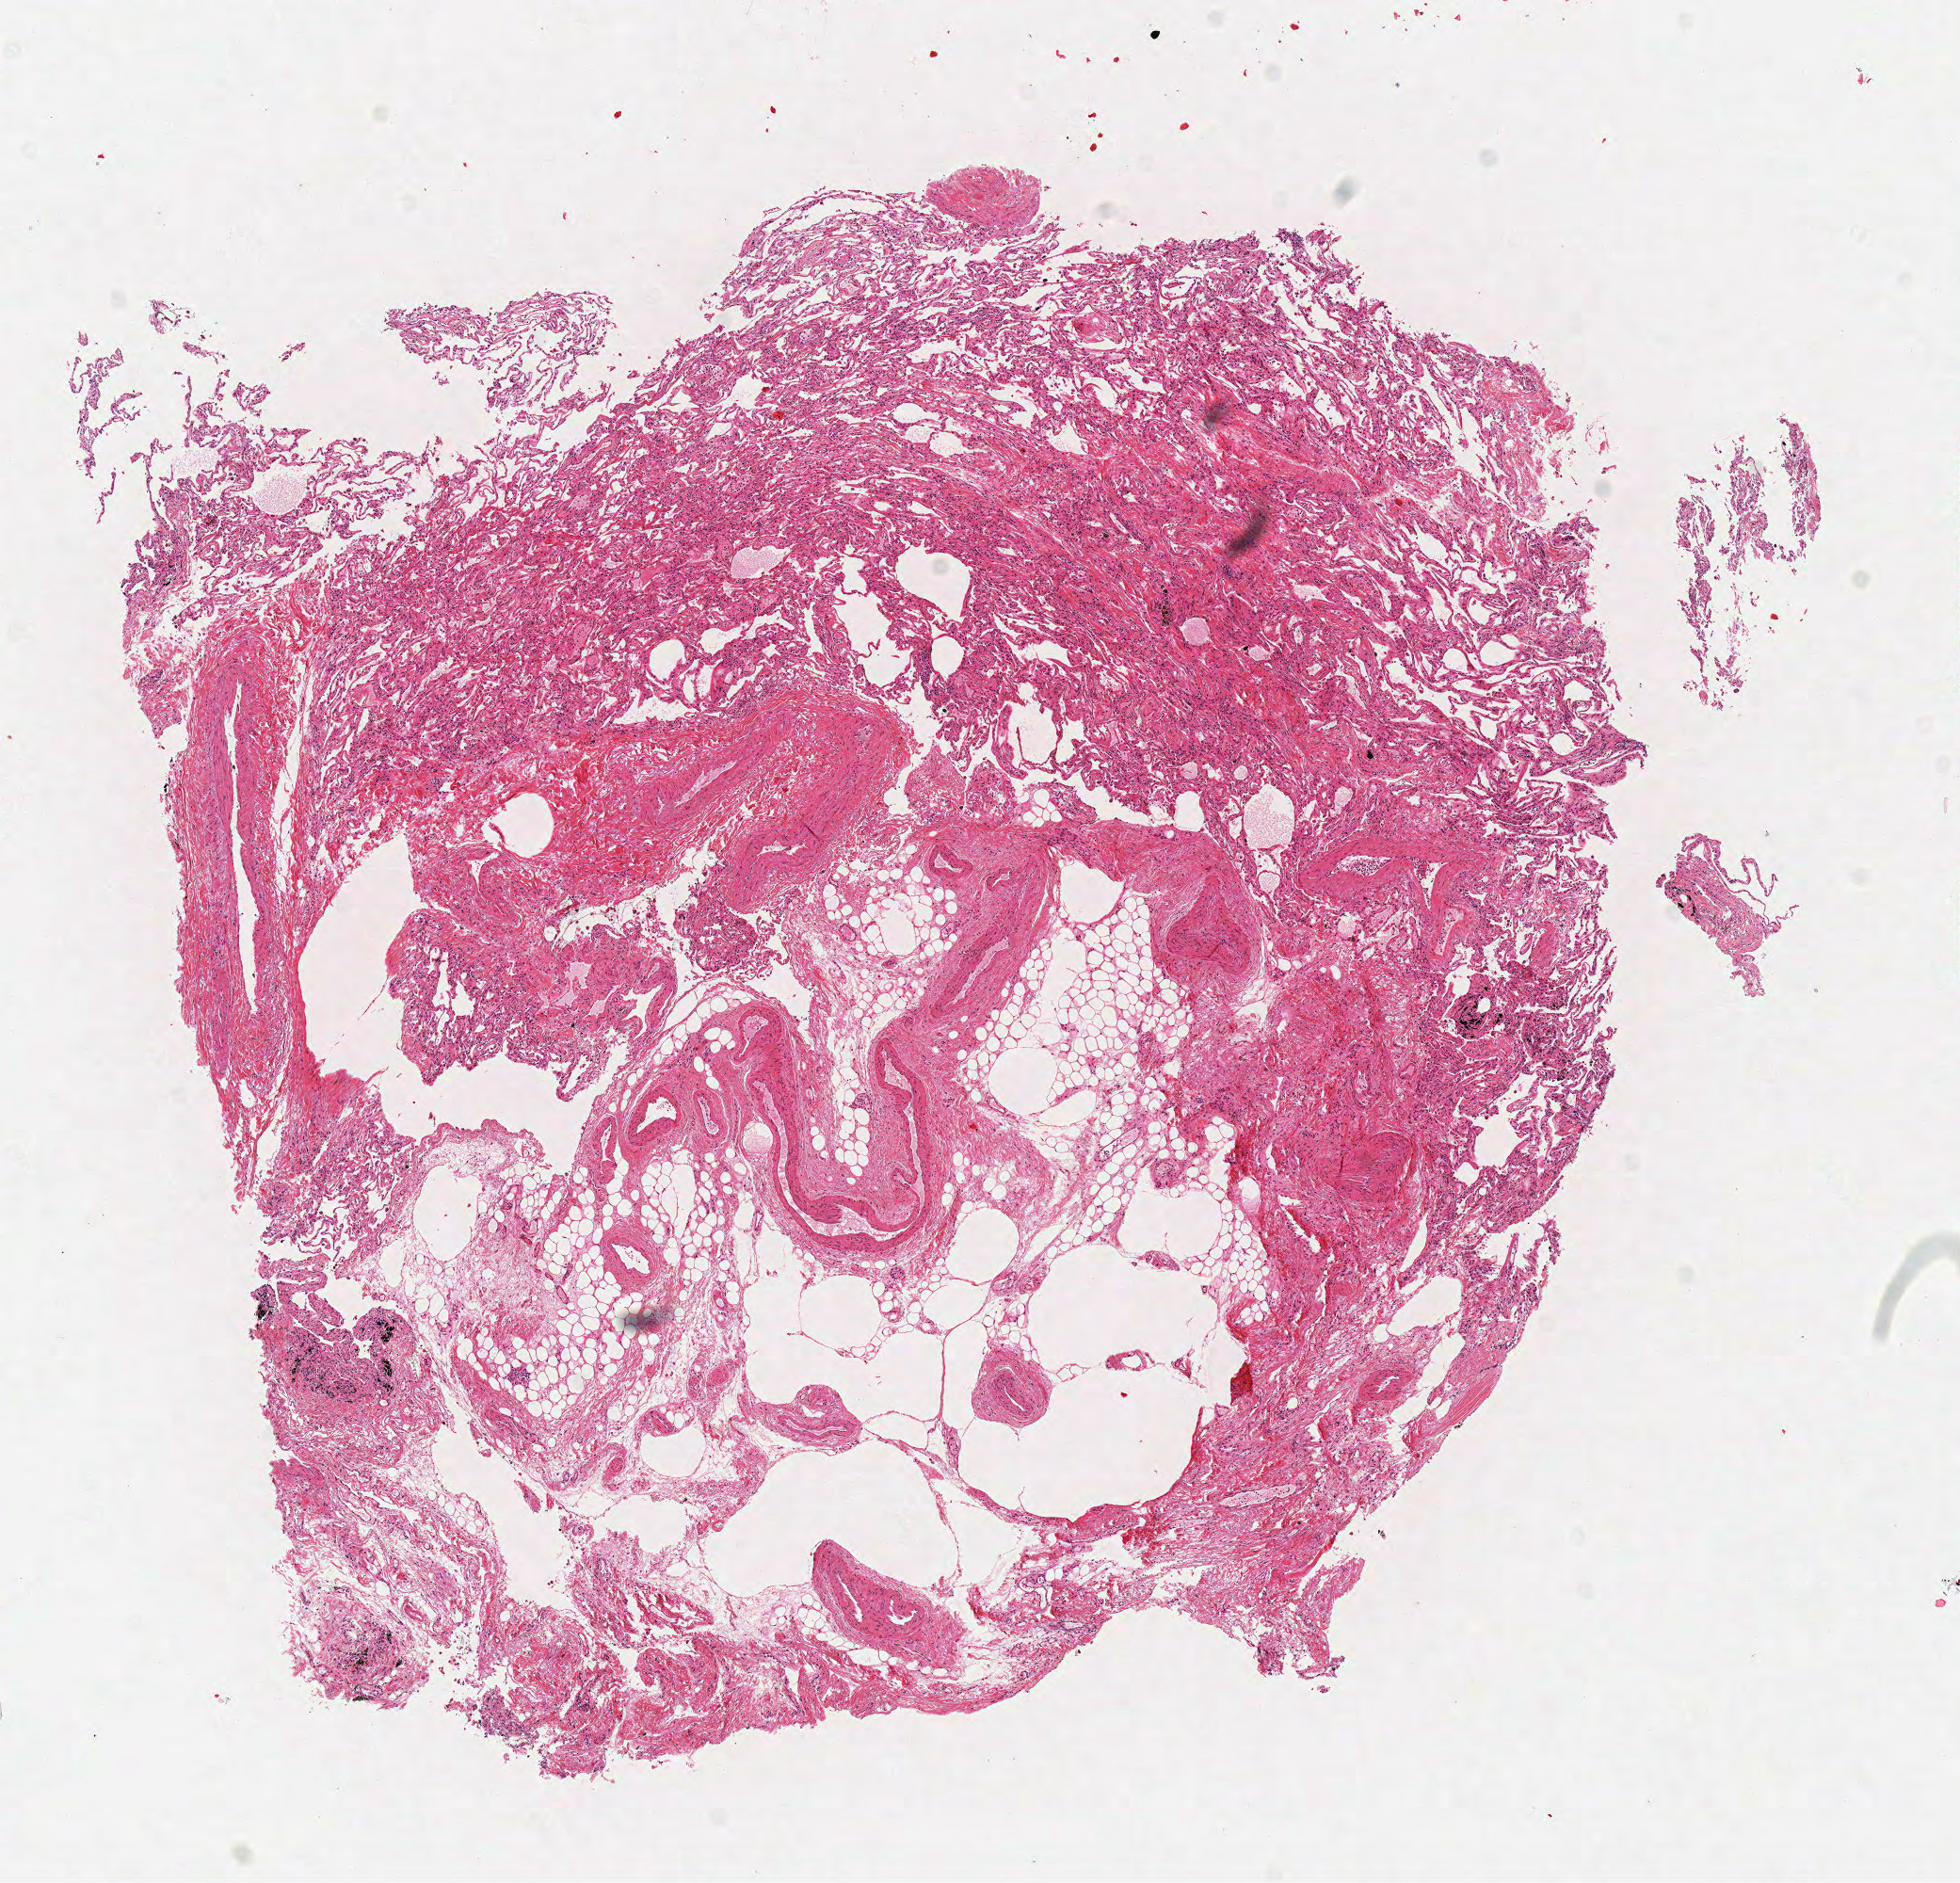
Hematoxylin and eosin (H&E) stained whole-slide image — whole scanned area (about 8.2 x 7.9 mm, from a 40x scan) shown as a low-resolution overview. Frozen section from the top of the tissue portion. Sample: solid tissue normal (non-tumour tissue), lung. Male, age 79 years at initial diagnosis.
This section: solid tissue normal sample (biorepository sample class). Patient diagnosis: Squamous cell carcinoma, NOS (overlapping lesion of lung).